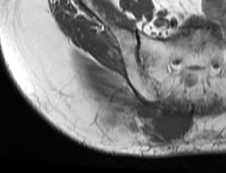
MRI of an extremity soft-tissue mass, one axial slice; position 52 of 73 along the scan axis; MR volume resampled by the dataset authors to the PET/CT grid (not the native acquisition matrix); 3.27 mm slice thickness; 226 × 173 image matrix. Female patient. From the clinical record (not read from this slice): histological type: spindle cell suggestive of myxofibrosarcoma; grade: intermediate; site of the primary tumour: right buttock.
Outlined on this slice (expert contour drawn on MRI and transferred to this co-registered scan by the dataset authors):
- gross tumour volume (mass): box from (x=91, y=94) to (x=190, y=146) px